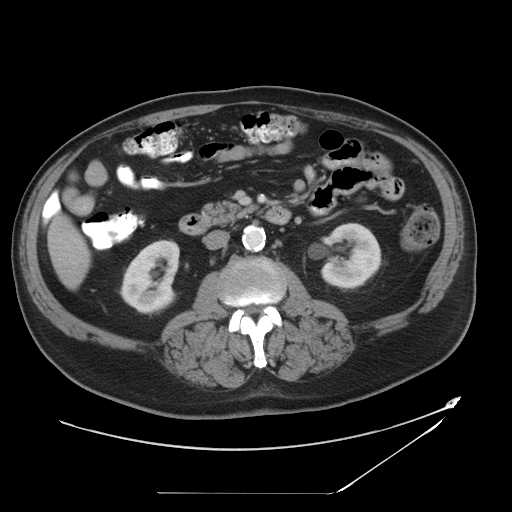
Contrast-enhanced abdominal CT, one axial slice; slice 13 of 49 in the series (ordered by position); reconstruction kernel STANDARD; intravenous contrast given; soft-tissue window (W 400 / L 40 HU); 5 mm slice thickness; 512 × 512 image matrix. Male patient, age 72 years. From the clinical record (not read from this slice): diagnosis: colorectal cancer liver metastases, imaged before liver resection; multiple liver metastases: no; largest metastasis: 2.5 cm; disease in both lobes: no.
Structures marked on this image (manually delineated by an expert):
- liver: bounding box <50,218,90,287> (left, top, right, bottom; pixels)
- planned liver remnant (the part of the liver to remain after resection): <50,218,90,287>